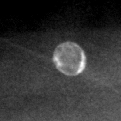
Region of interest cut from a scanned film mammogram (one marked finding); right breast; CC view.
Calcifications, morphology lucent center; BI-RADS assessment category 2; subtlety rating 5 on a 1 (subtle) to 5 (obvious) scale; benign without callback (not worked up further).